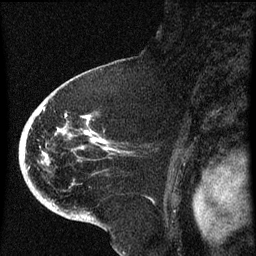
Breast MRI (dynamic contrast-enhanced), one sagittal slice; slice 44 of 60 in the series (ordered by position); dynamic contrast-enhanced series, image 2 of 4 at this slice position (ordered by acquisition); 1.5 T; TE 4.2 ms, TR 8 ms; 2 mm slice thickness; 256 × 256 image matrix. Female patient, age 71 years.
Annotated regions visible in this slice (semi-automatic segmentation, software-assisted and operator-edited):
- analysis volume of interest (the breast-tissue region the enhancement analysis was run in; not a lesion): bounding box (x1, y1, x2, y2) in pixels: (32, 86, 130, 205)
- tumour enhancement mask (voxels above the 70 % enhancement threshold inside the analysis volume of interest): (43, 108, 119, 153)